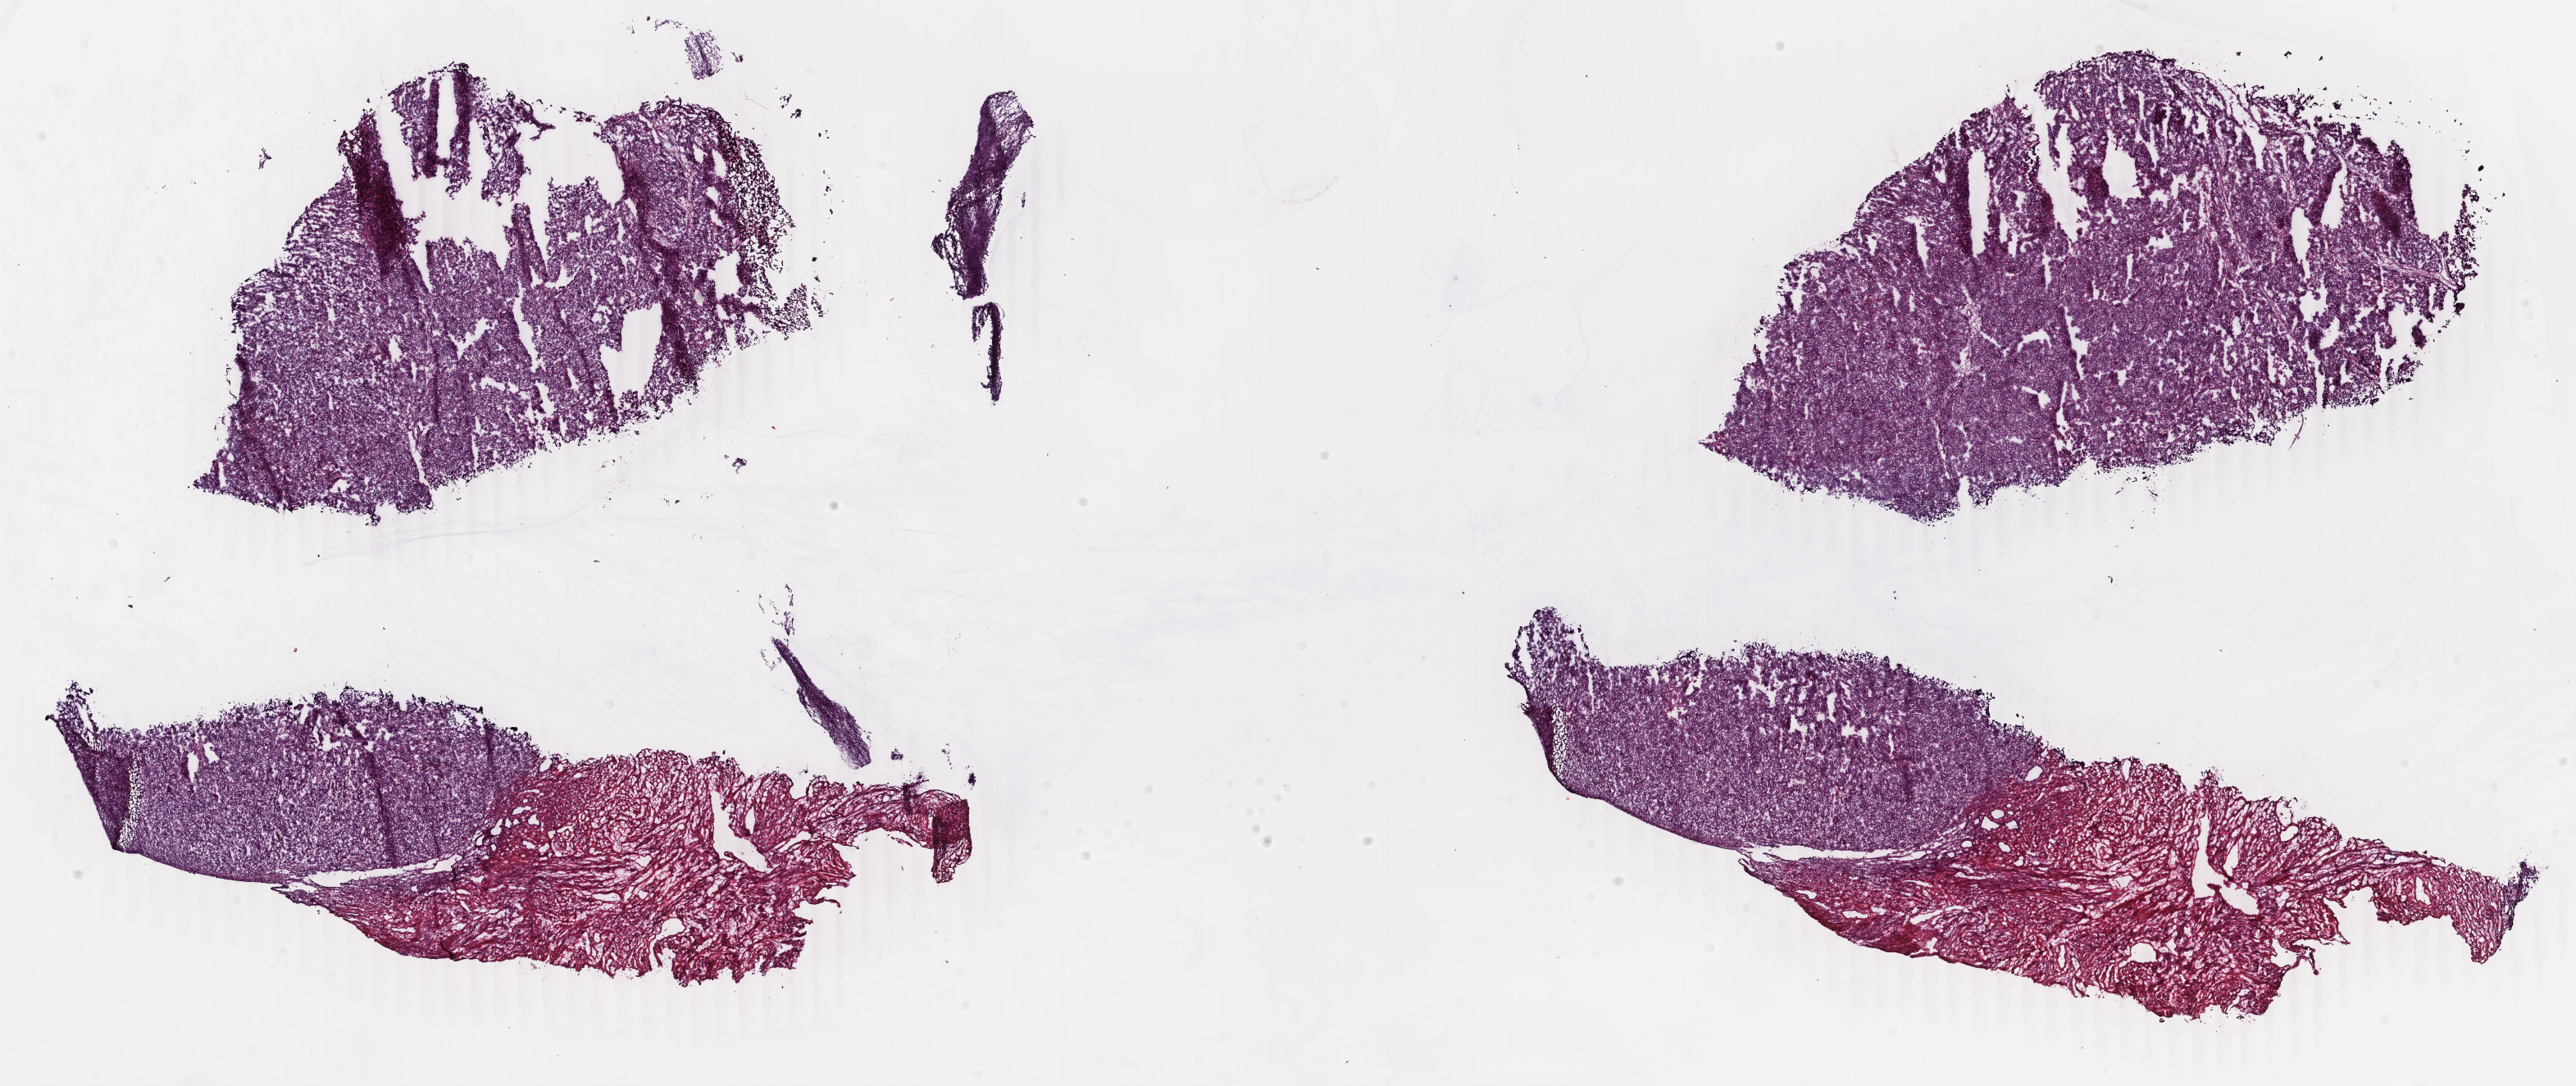
H&E-stained whole-slide image, low-resolution overview of the scanned area, about 25.0 x 10.5 mm; frozen section; uterus, primary tumour sample. Patient sex: female. Histologic grade: G3 (poorly differentiated). Composition of this section per pathologist review: tumour cells 60%, tumour nuclei 70%, normal cells 30%, stromal cells 2%, necrosis 8%. Infiltration values recorded for this section: lymphocyte infiltration 0%, monocyte infiltration 0%, neutrophil infiltration 0%.
* FIGO stage: IA
* pathologic diagnosis: Endometrioid adenocarcinoma, NOS (endometrium)